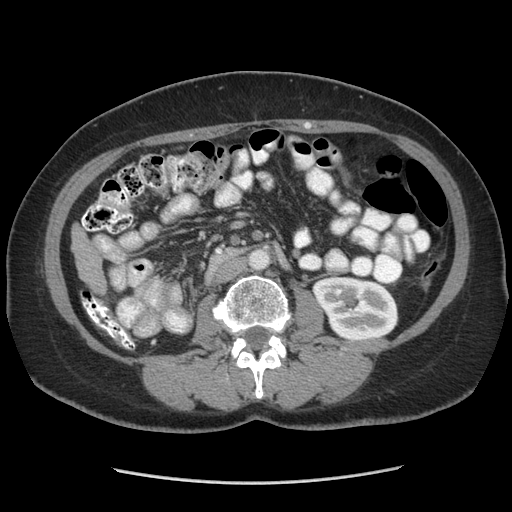
Contrast-enhanced abdominal CT (liver protocol), one axial slice. Position 111 of 185 along the scan axis. Reconstruction kernel STANDARD. Soft-tissue window (W 400 / L 40 HU). 2.5 mm slice thickness. 512 × 512 image matrix, field of view 360 × 360 mm. Case-level facts recorded for this patient, not image findings: diagnosis: hepatocellular carcinoma (patient treated with transarterial chemoembolisation; whether this scan precedes or follows treatment is not stated here); TNM stage (as recorded): Stage-I; Child-Pugh class: A; tumour differentiation: poorly differentiated; tumour nodularity: uninodular.
Structures marked on this image (semi-automatic segmentation, software-assisted and operator-edited):
- liver parenchyma outside the tumour (the mass and vessels are separate outlines, so this box may not span the whole liver): bounding box (x1, y1, x2, y2) in pixels: (72, 224, 106, 292)